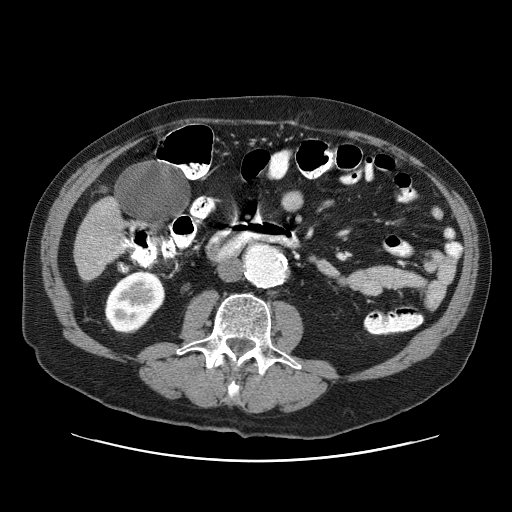
Contrast-enhanced abdominal CT (liver protocol), one axial slice; one of 3 acquisitions stored at this slice position; soft-tissue window (W 400 / L 40 HU); 2.5 mm slice thickness; 512 × 512 image matrix. From the clinical record (not read from this slice): diagnosis: hepatocellular carcinoma (patient treated with transarterial chemoembolisation; whether this scan precedes or follows treatment is not stated here); TNM stage (as recorded): Stage-IIIA; Child-Pugh class: A; tumour differentiation: well differentiated.
Annotated regions visible in this slice (semi-automatic segmentation, software-assisted and operator-edited):
- liver parenchyma outside the tumour (the mass and vessels are separate outlines, so this box may not span the whole liver): bounding box [x1, y1, x2, y2] px = [74, 196, 124, 280]